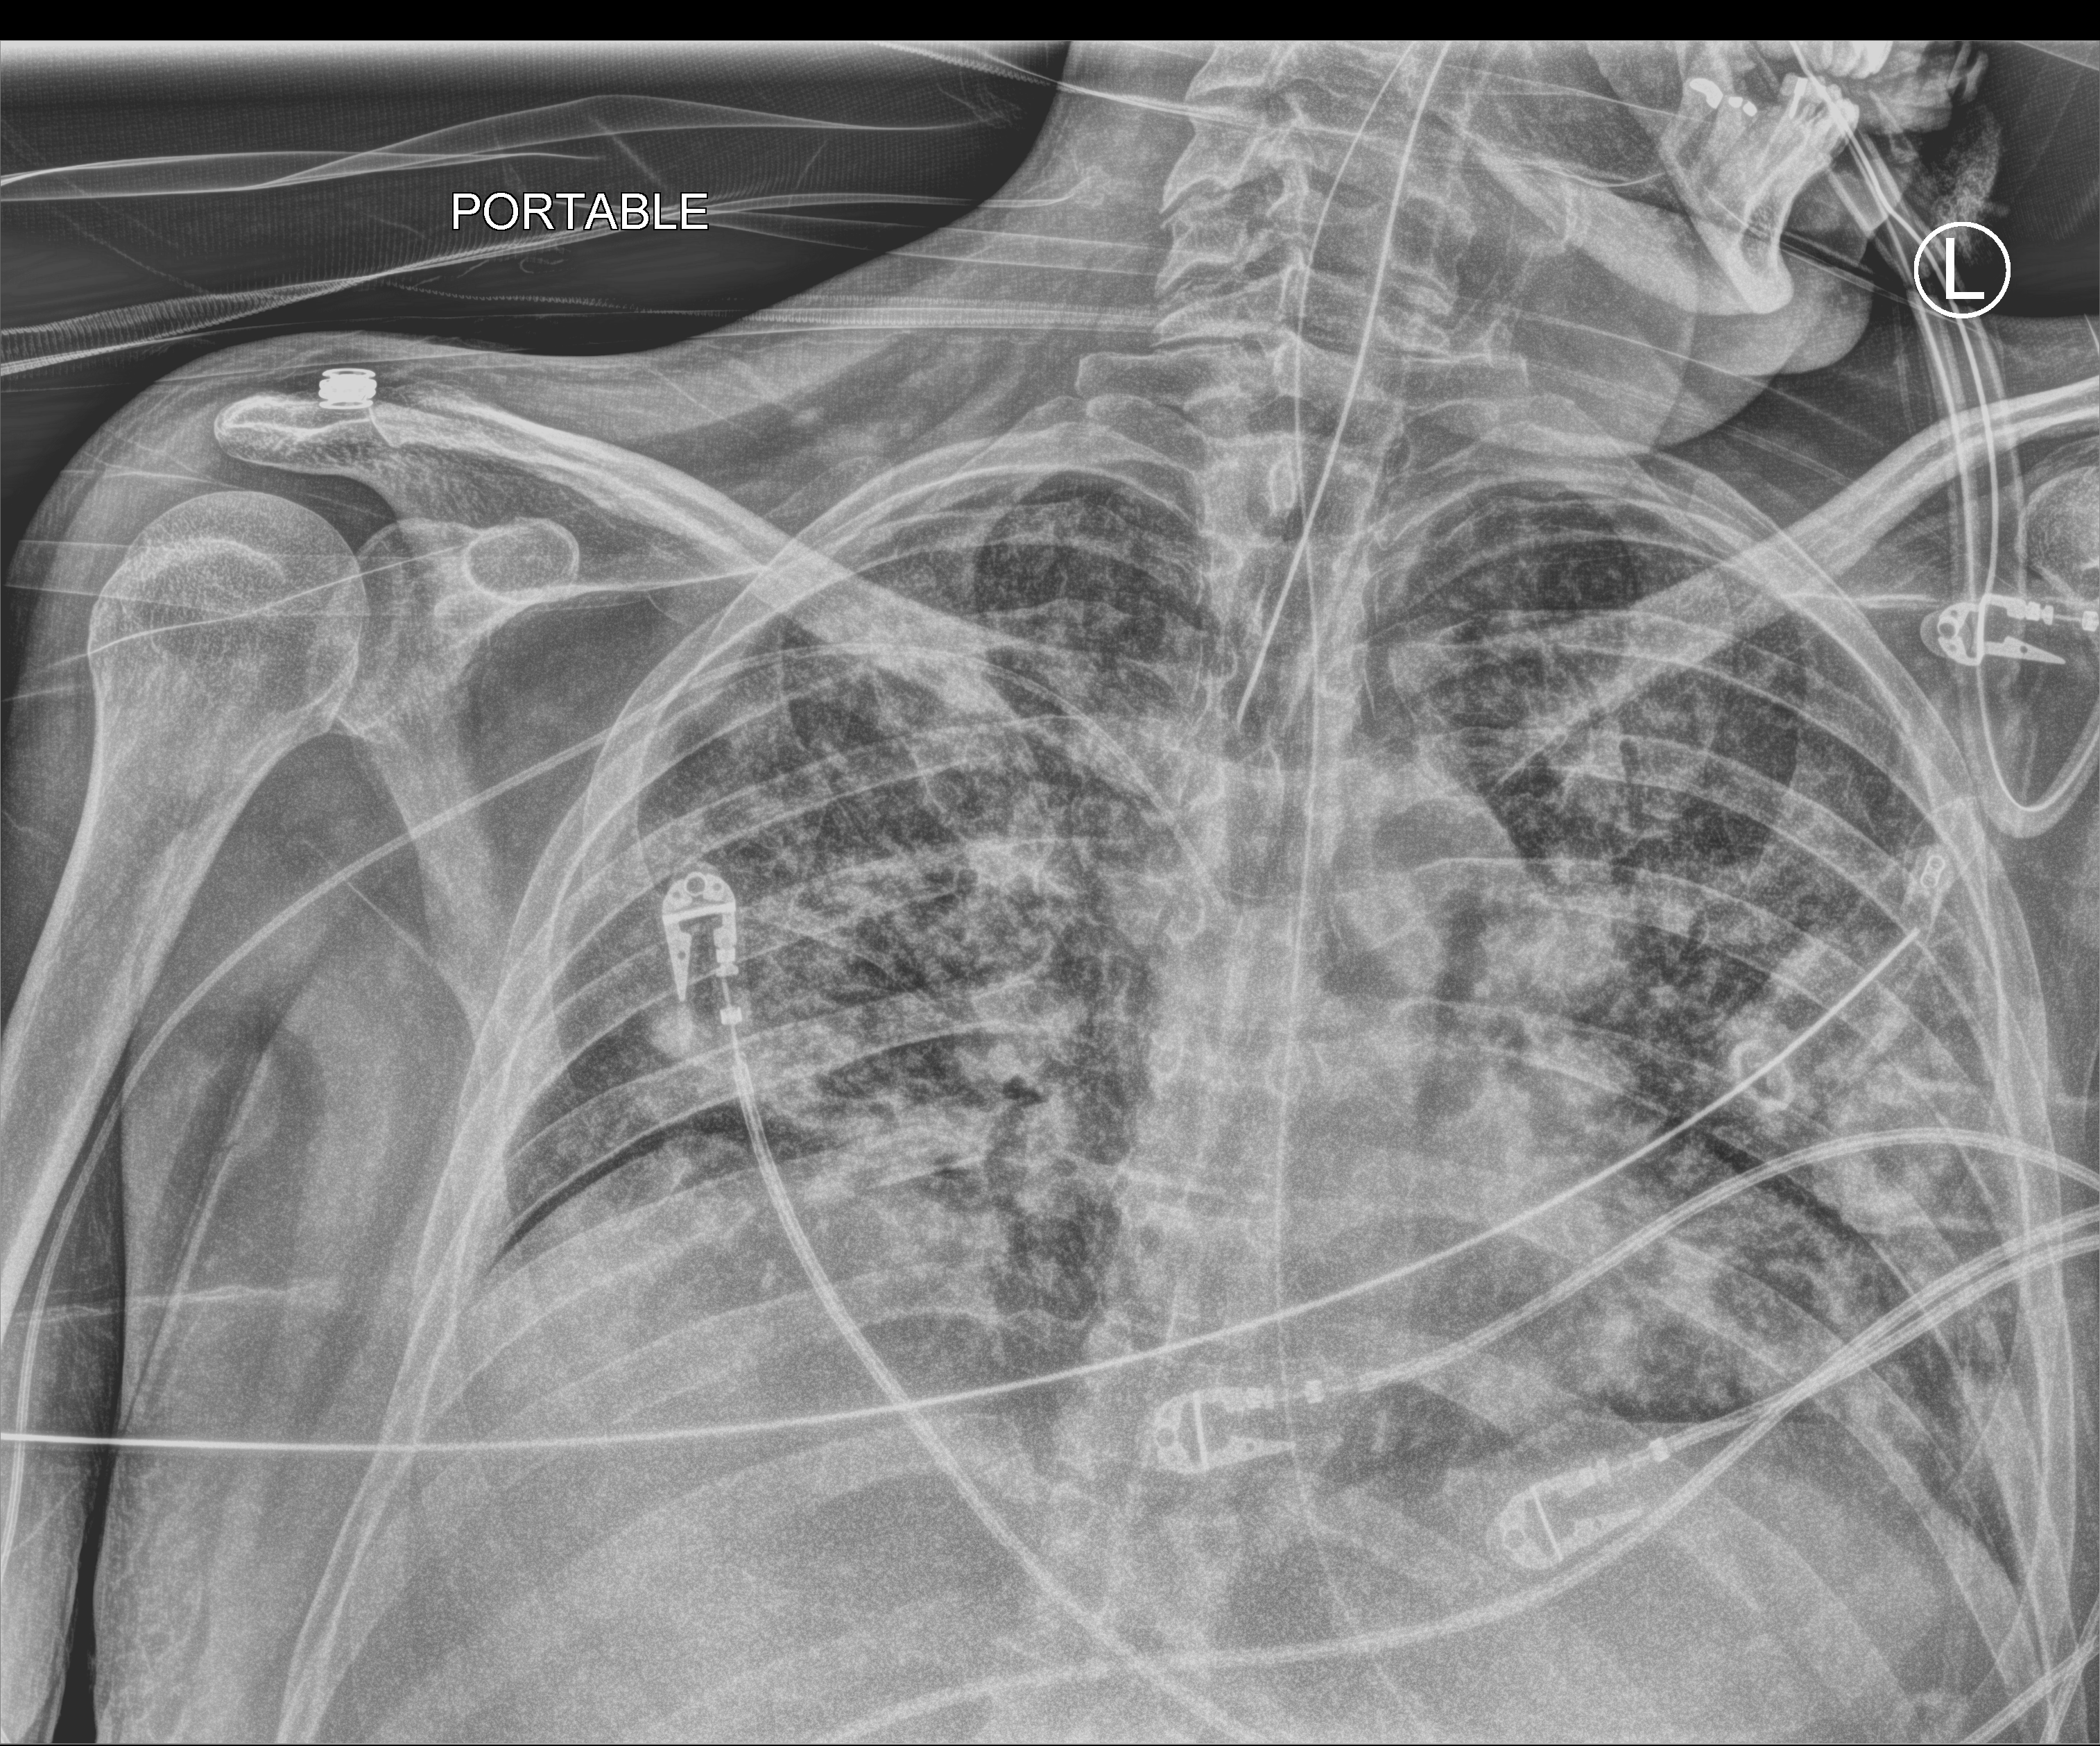
Portable chest radiograph, anteroposterior (AP) projection. Patient hospitalised with COVID-19; male, aged 18–59 years.
From the hospital-stay record, not from the radiograph (when in the stay this image was taken is not recorded): other chronic lung disease (admission record): no.